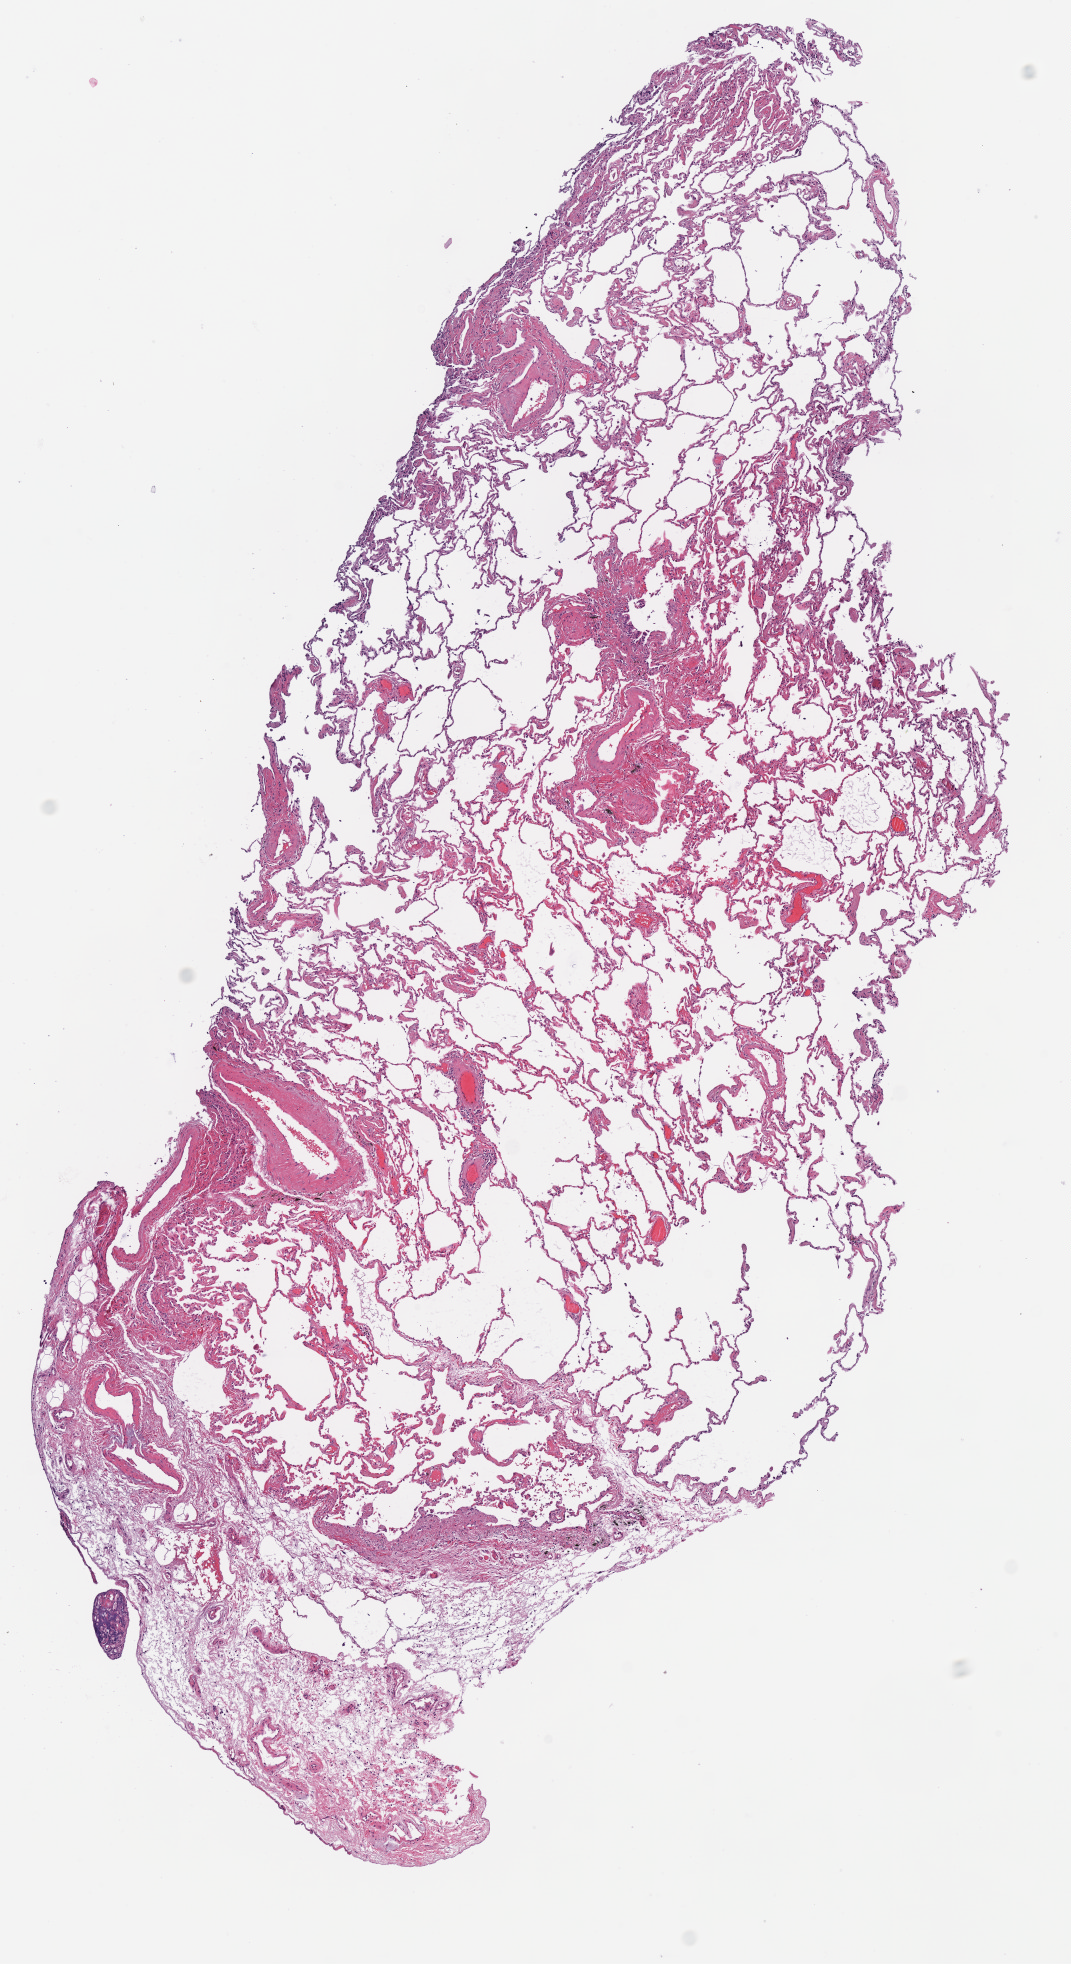
Whole-slide histology image, Hematoxylin and eosin (H&E) stained, a low-resolution overview of the entire scanned area, about 4.2 x 7.7 mm (acquisition: 40x scan); frozen section from the top of the tissue portion; solid tissue normal (non-tumour tissue) sample from the lung. Male patient; age at initial diagnosis 73 years.
This section: solid tissue normal sample (biorepository sample class). Patient diagnosis: Squamous cell carcinoma, NOS (upper lobe, lung).